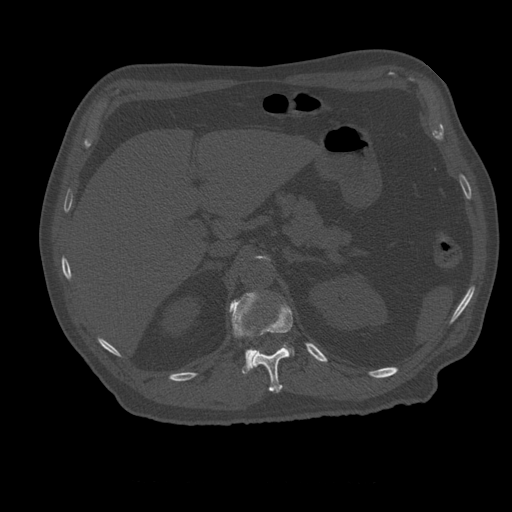
CT including the spine, one axial slice; slice 254 of 399 in the series (ordered by position); reconstruction kernel STANDARD; 120 kVp; bone window (W 1800 / L 400 HU); 1.25 mm slice thickness; 512 × 512 image matrix, field of view 407 × 407 mm. Patient age 73 years. Case-level facts recorded for this patient, not image findings: primary cancer: prostate; vertebrae with lytic lesions (as recorded): L2.
Structures marked on this image (semi-automatic segmentation, software-assisted and operator-edited):
- L1 vertebra: box from (x=230, y=292) to (x=295, y=375) px
- T12 vertebra: (x=251, y=304)–(x=293, y=393)